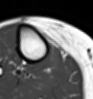
MRI of an extremity soft-tissue mass, one axial slice; position 32 of 54 along the scan axis; MR volume resampled by the dataset authors to the PET/CT grid (not the native acquisition matrix); 3.27 mm slice thickness; 93 × 99 image matrix. Female patient. Case-level facts recorded for this patient, not image findings: histological type: undifferentiated – high grade; grade: high; site of the primary tumour: right thigh.
Structures marked on this image (expert contour drawn on MRI and transferred to this co-registered scan by the dataset authors):
- gross tumour volume (mass): bounding box (x1, y1, x2, y2) in pixels: (45, 45, 64, 71)